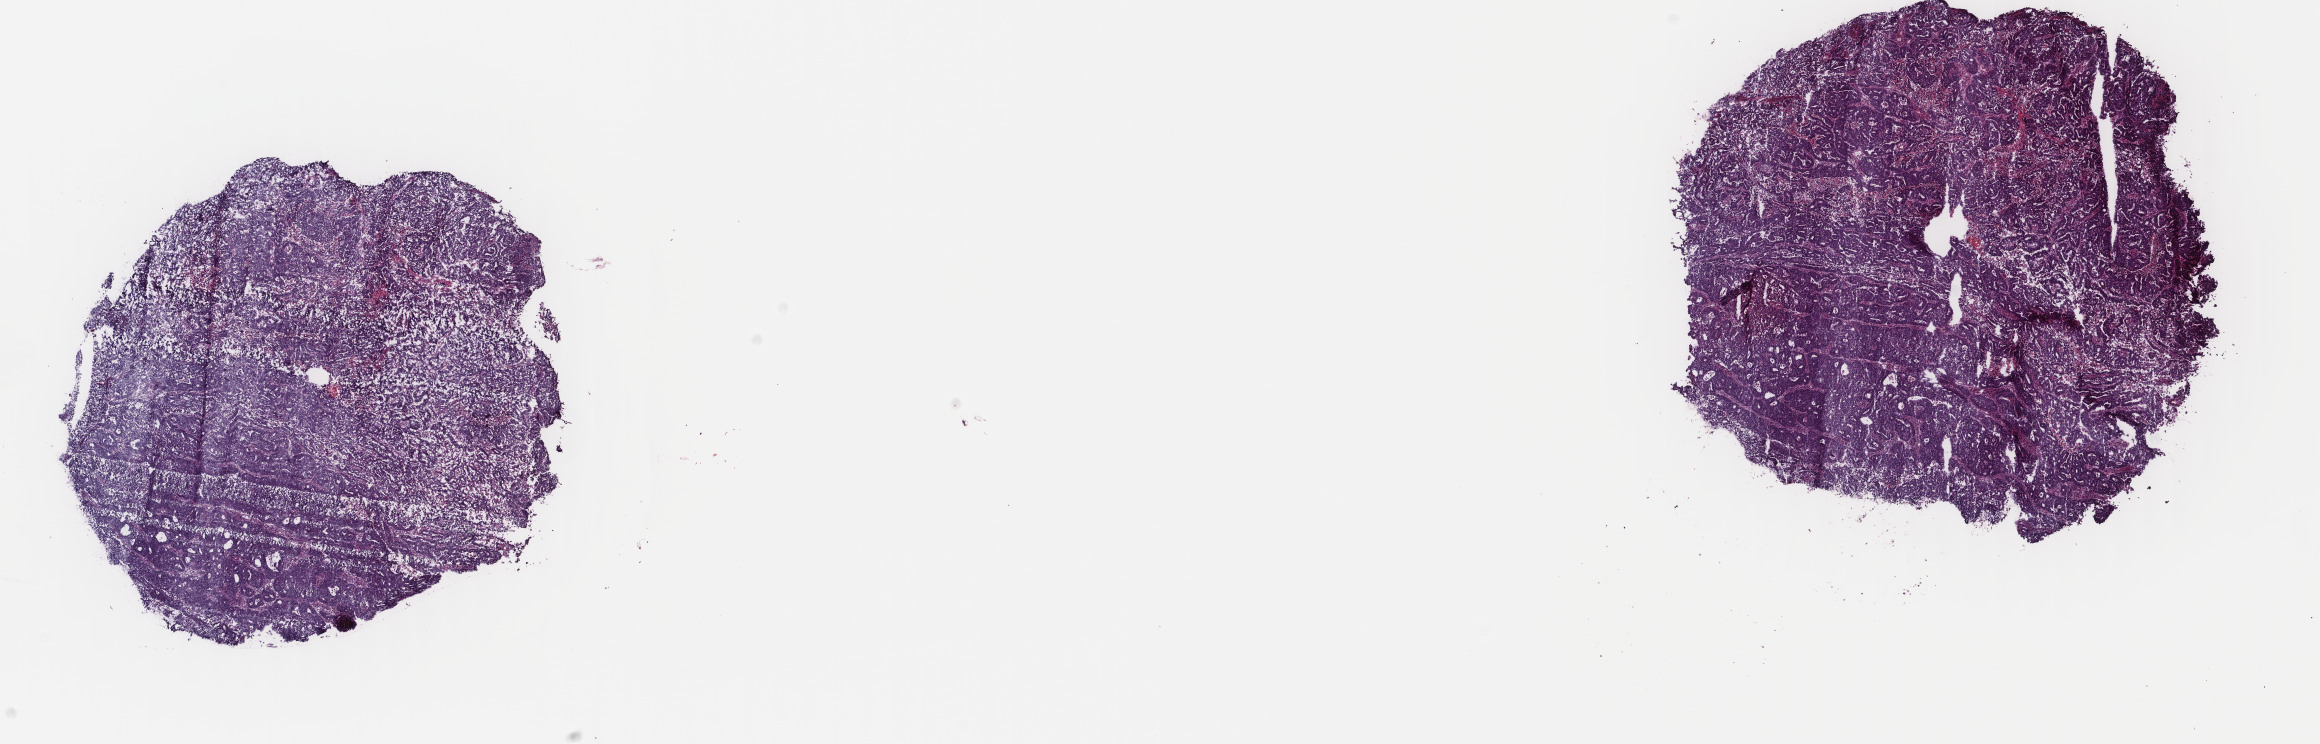
Digitized Hematoxylin and eosin (H&E) stained tissue section (whole slide), a low-resolution overview of the entire scanned area, about 18.4 x 5.9 mm (acquisition: 40x scan), frozen section from the top of the tissue portion, sample: primary tumour, uterus. Patient: female, age at initial diagnosis 71 years. Histologic grade: G3 (poorly differentiated). Composition of this section per pathologist review: tumour cells 70%, tumour nuclei 90%, normal cells 0%, stromal cells 10%, necrosis 20%. Inflammatory infiltration, as recorded: lymphocyte infiltration 20%, monocyte infiltration 0%, neutrophil infiltration 10%.
• FIGO stage: IB
• diagnosis: Endometrioid adenocarcinoma, NOS